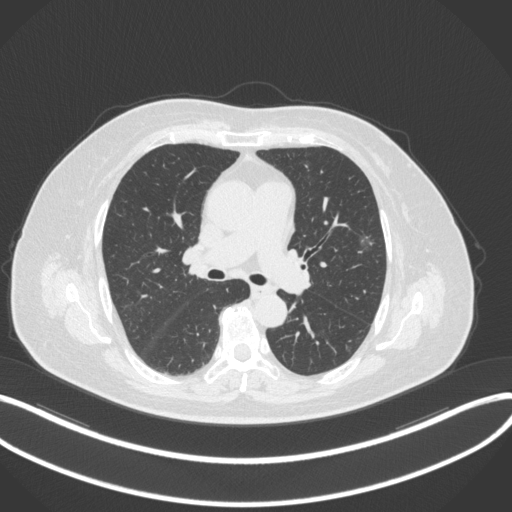
Chest CT, one axial slice. Slice 187 of 286 in the series (ordered by position). Reconstruction kernel B31f. 120 kVp. Lung window (W 1500 / L -600 HU). 512 × 512 image matrix, field of view 400 × 400 mm. Female patient, age 76 years. Case-level facts recorded for this patient, not image findings: clinical TNM (as recorded): T1b N0 M0.
Annotated regions visible in this slice (bounding box drawn by a radiologist):
- lung tumour (recorded histology: adenocarcinoma): box from (x=351, y=228) to (x=376, y=260) px